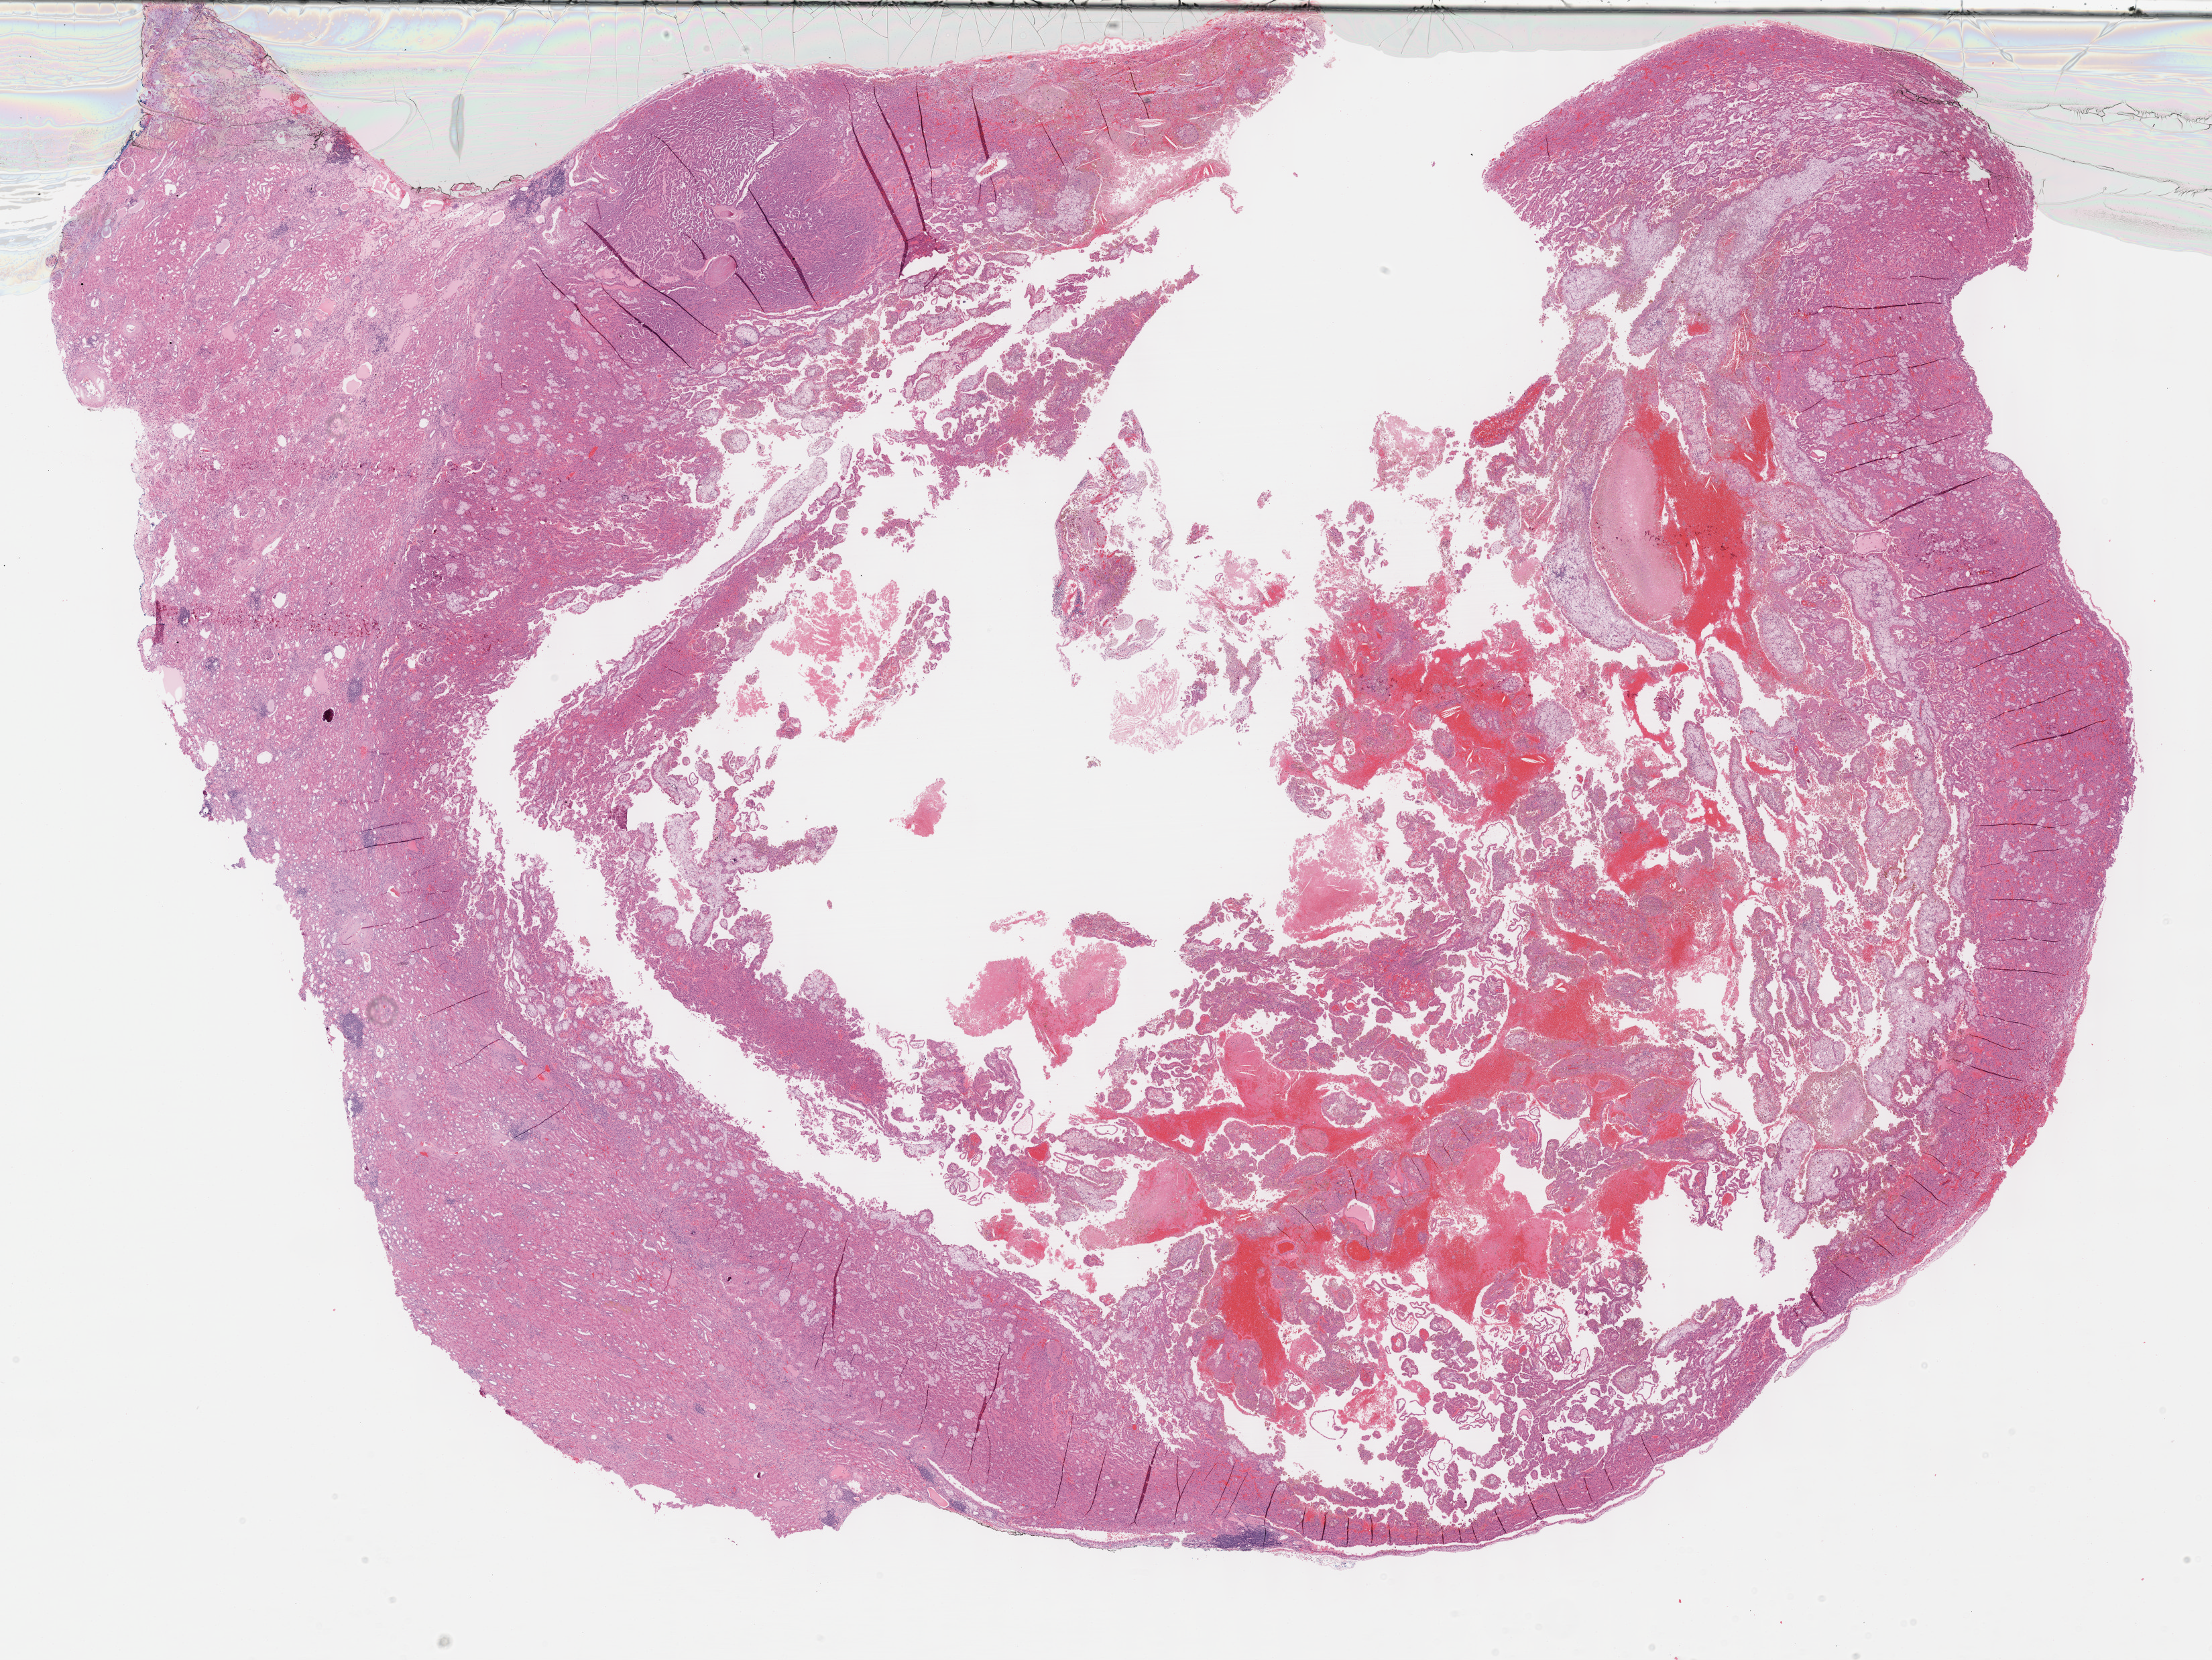
Digitized H&E tissue section (whole slide) — a low-resolution overview of the entire scanned area, about 26.7 x 20.0 mm (acquisition: 40x scan), formalin-fixed paraffin-embedded (FFPE) diagnostic section, sample: primary tumour, kidney. Patient: male, age at initial diagnosis 80 years.
* pathologic diagnosis: Papillary adenocarcinoma, NOS
* AJCC pathologic stage: I (6th edition)